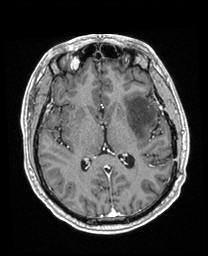
Brain MRI from a brain-tumour surgery series, one axial slice; position 105 of 208 along the scan axis; T1-weighted post-contrast; 208 × 256 image matrix, field of view 211 × 260 mm. From the clinical record (not read from this slice): histopathology: Astrocytoma; WHO grade: 3; IDH mutation: yes.
Outlined on this slice (expert manual segmentation):
- previous resection cavity: bounding box (x1, y1, x2, y2) in pixels: (150, 124, 162, 139)